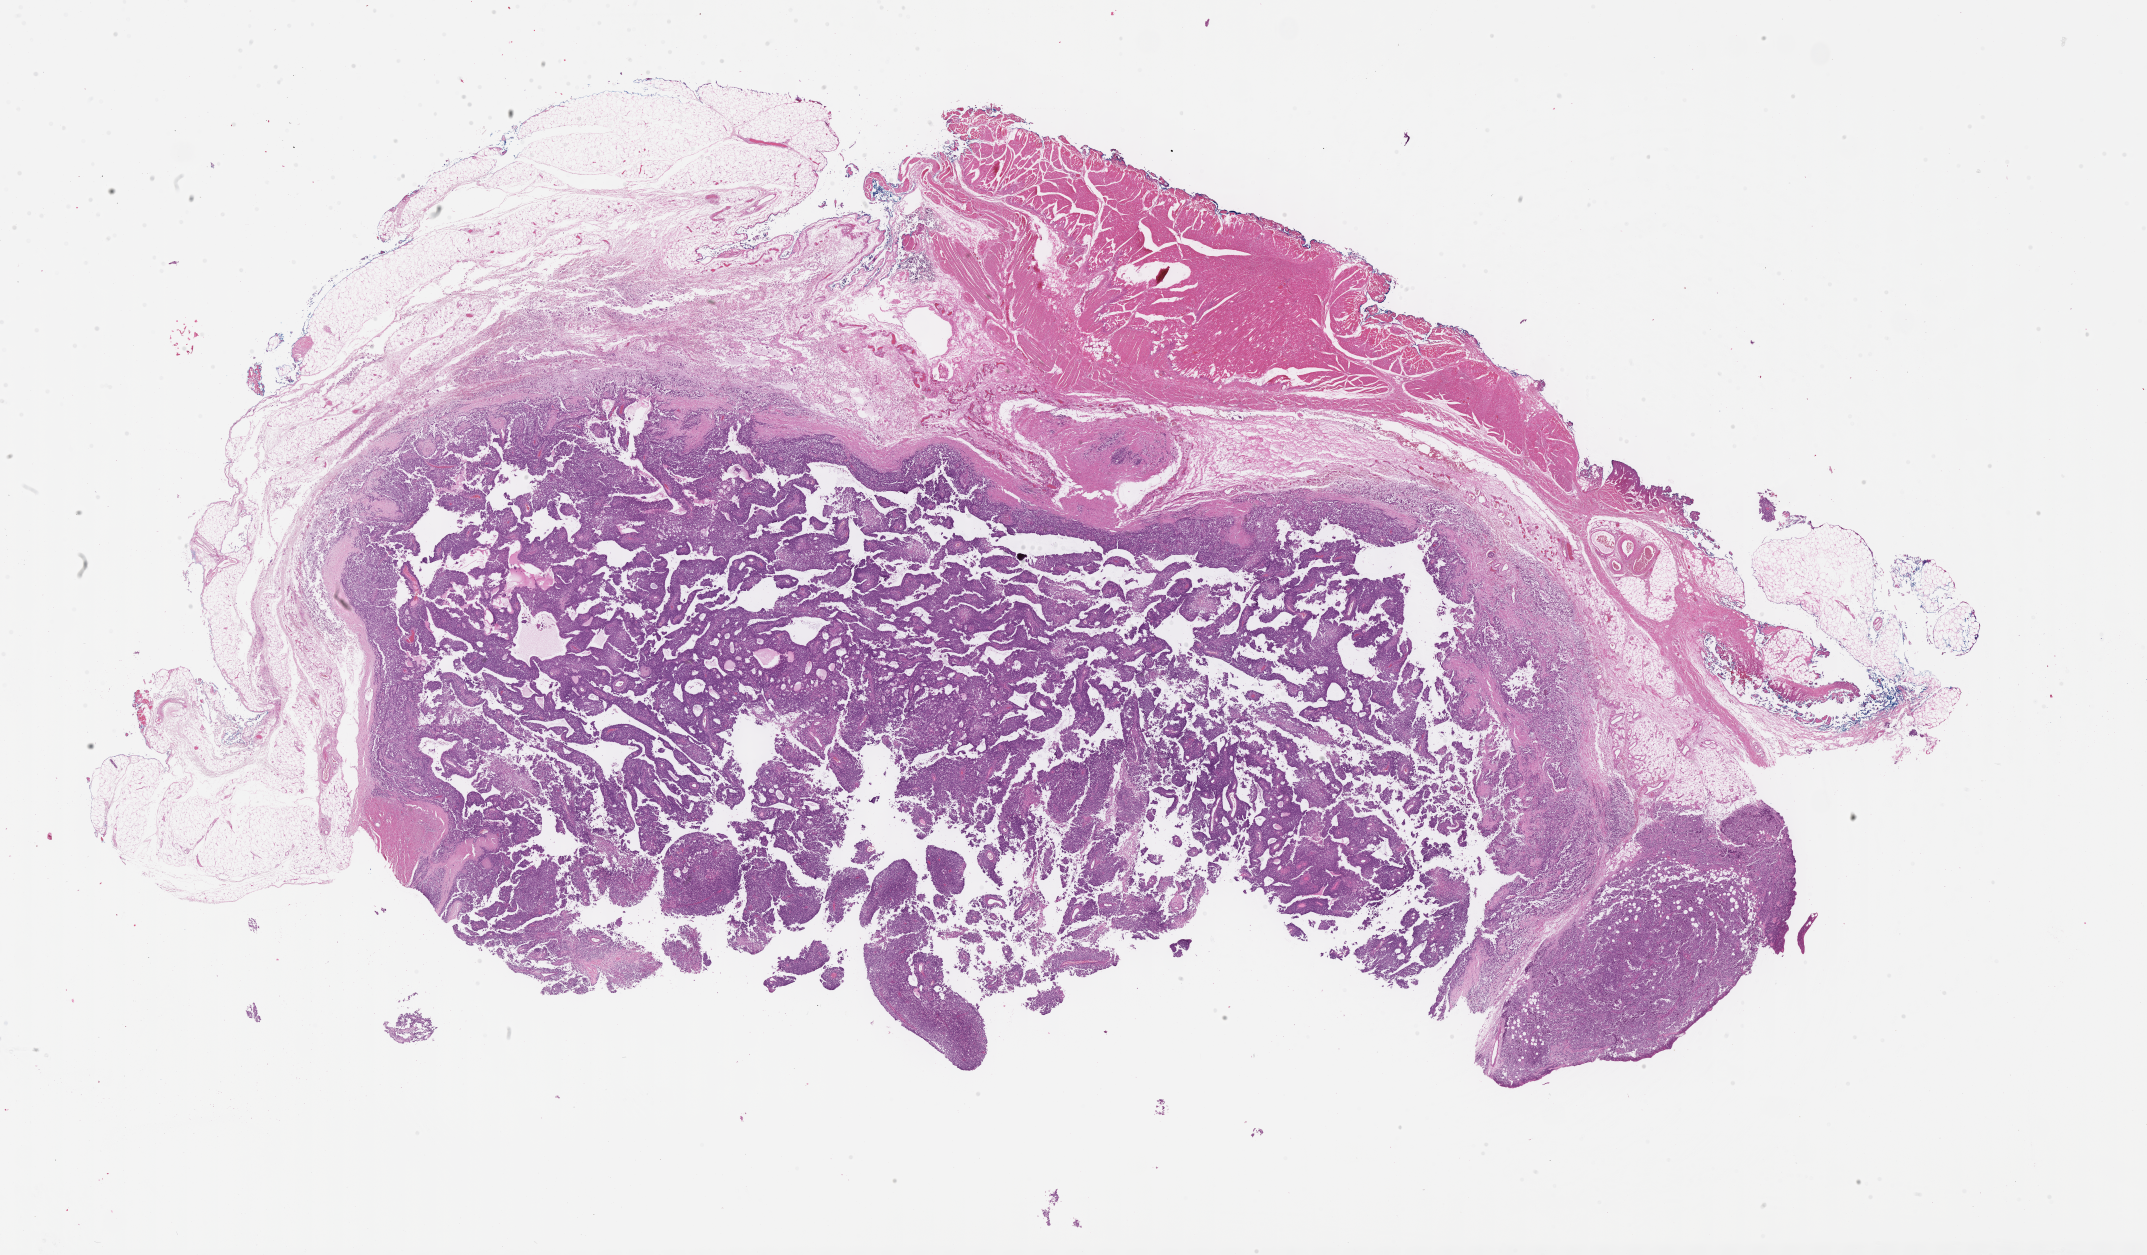
Digitized H&E-stained section of tumor tissue — a low-resolution overview of the entire scanned area, about 34.7 x 20.3 mm, formalin-fixed, paraffin-embedded (FFPE) tissue, sample anatomic site: thigh, left. Male patient, age at diagnosis 1.2 years.
• diagnosis: rhabdomyosarcoma; histological classification: alveolar rhabdomyosarcoma
• metastatic status at presentation (as recorded): non-metastatic
• stage (as recorded): 3